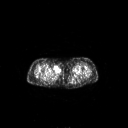
FDG PET of an extremity soft-tissue mass (from a PET/CT study), one axial slice. Position 237 of 311 along the scan axis. 3.27 mm slice thickness. 128 × 128 image matrix, field of view 700 × 700 mm. Patient: female, 78 years. From the clinical record (not read from this slice): histological type: leiomyosarcoma; grade: intermediate; site of the primary tumour: parascapusular.
Structures marked on this image (expert contour drawn on MRI and transferred to this co-registered scan by the dataset authors):
- gross tumour volume including surrounding oedema: box from (x=52, y=66) to (x=62, y=75) px
- gross tumour volume (mass): (x=52, y=66)–(x=62, y=75)